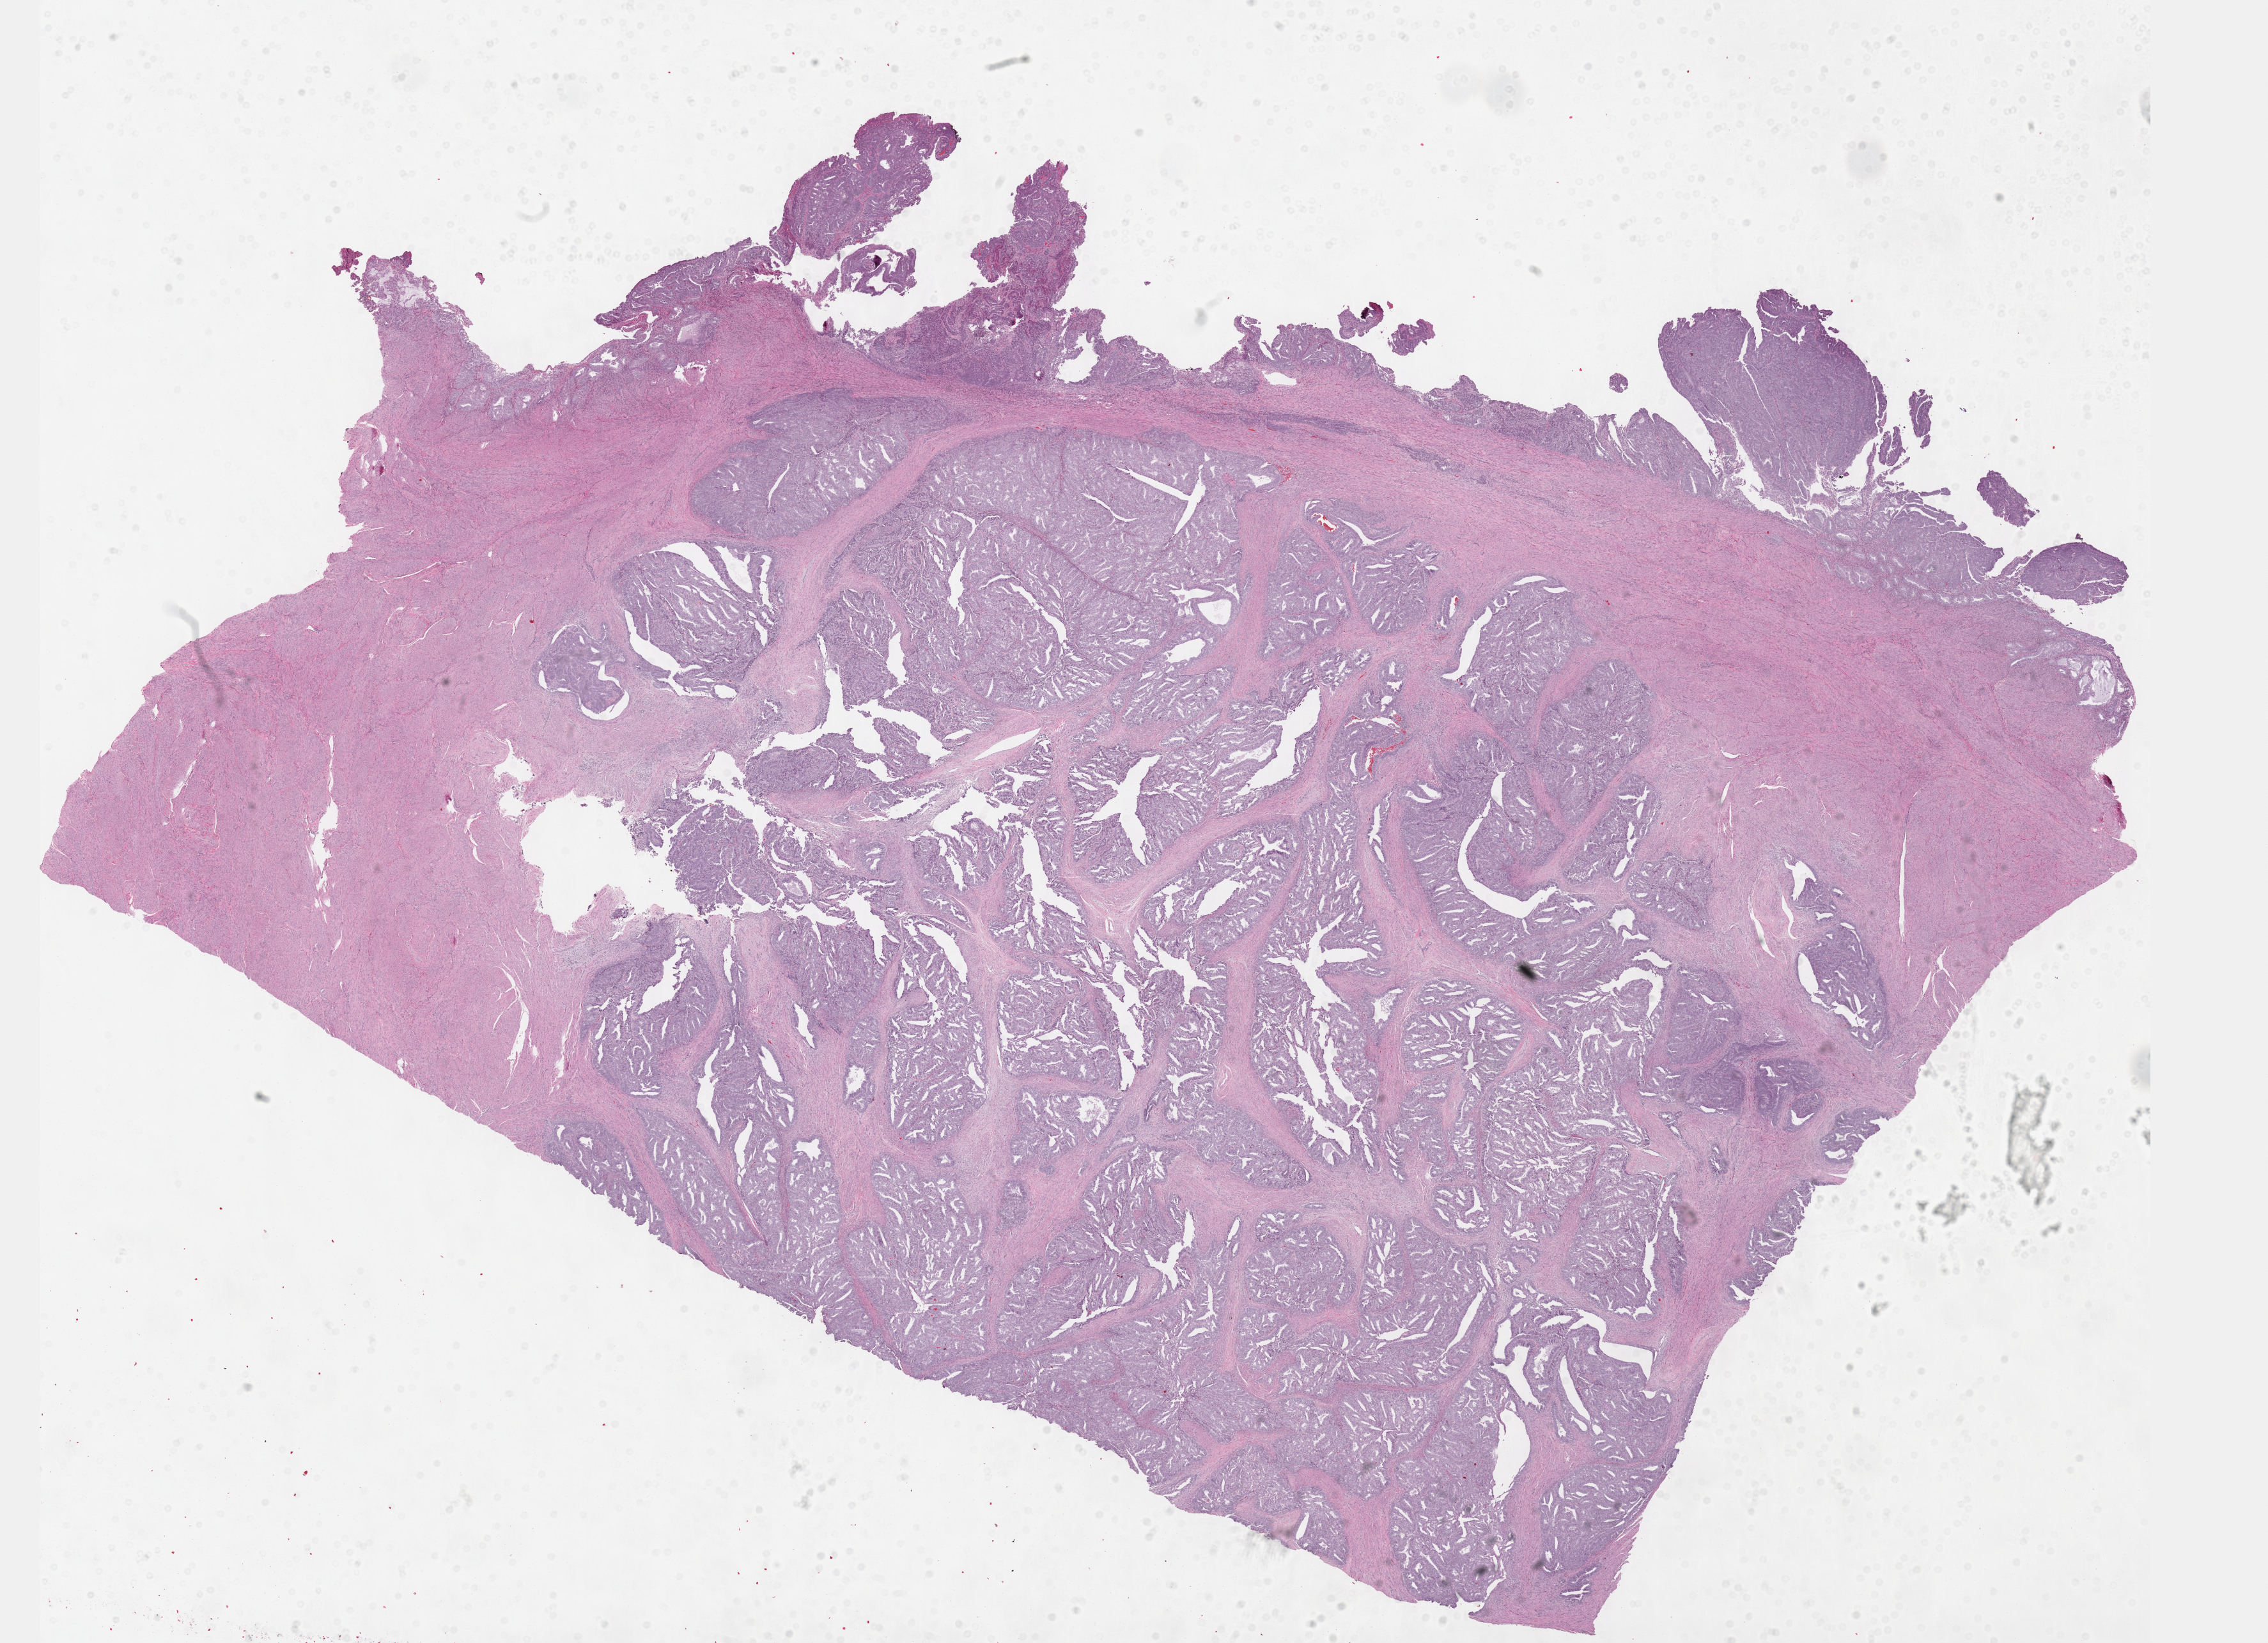
Whole-slide histology image, H&E — a low-resolution overview of the entire scanned area, about 28.7 x 20.8 mm (acquisition: 40x scan); formalin-fixed paraffin-embedded (FFPE) diagnostic section; primary tumour sample from the uterus. Patient: female, age at initial diagnosis 61 years. Histologic grade: G2 (moderately differentiated).
FIGO stage: IB. Diagnosis: Endometrioid adenocarcinoma, NOS.